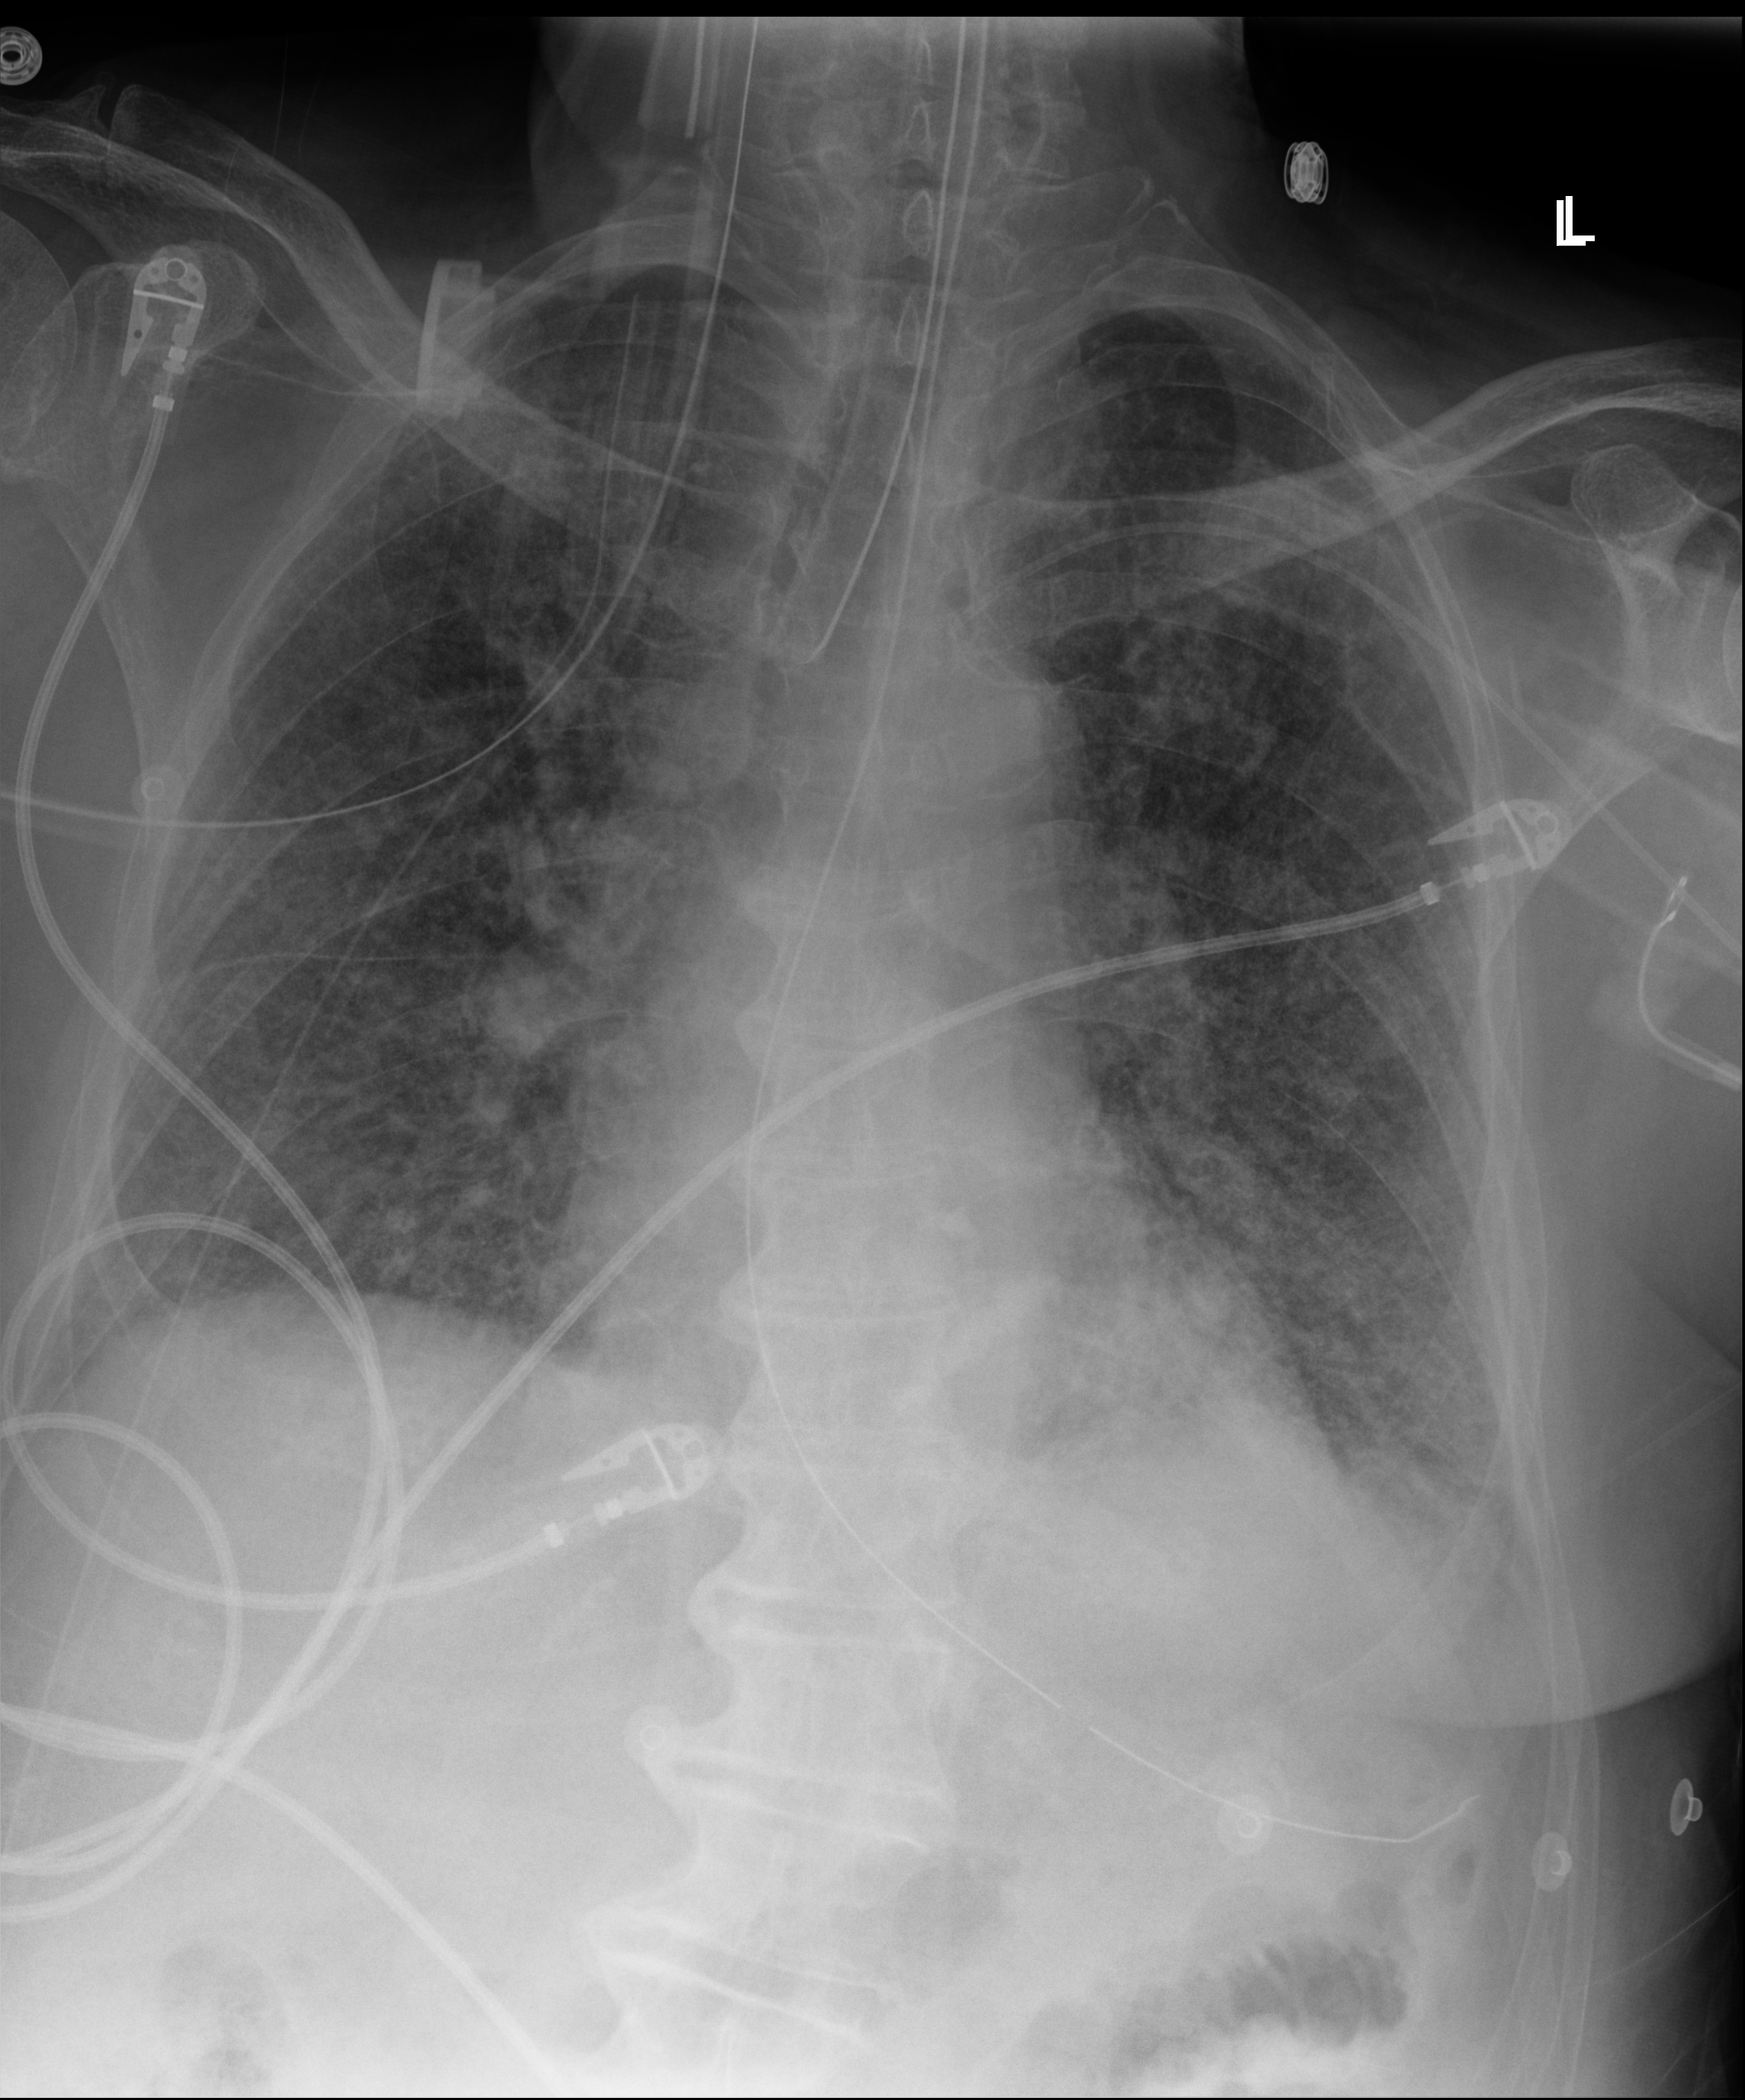
Chest X-ray, anteroposterior (AP) projection. Patient hospitalised with COVID-19; male, aged 75–90 years.
From the hospital-stay record, not from the radiograph (when in the stay this image was taken is not recorded): smoking status (admission record): never; mechanically ventilated during this hospital stay: yes.